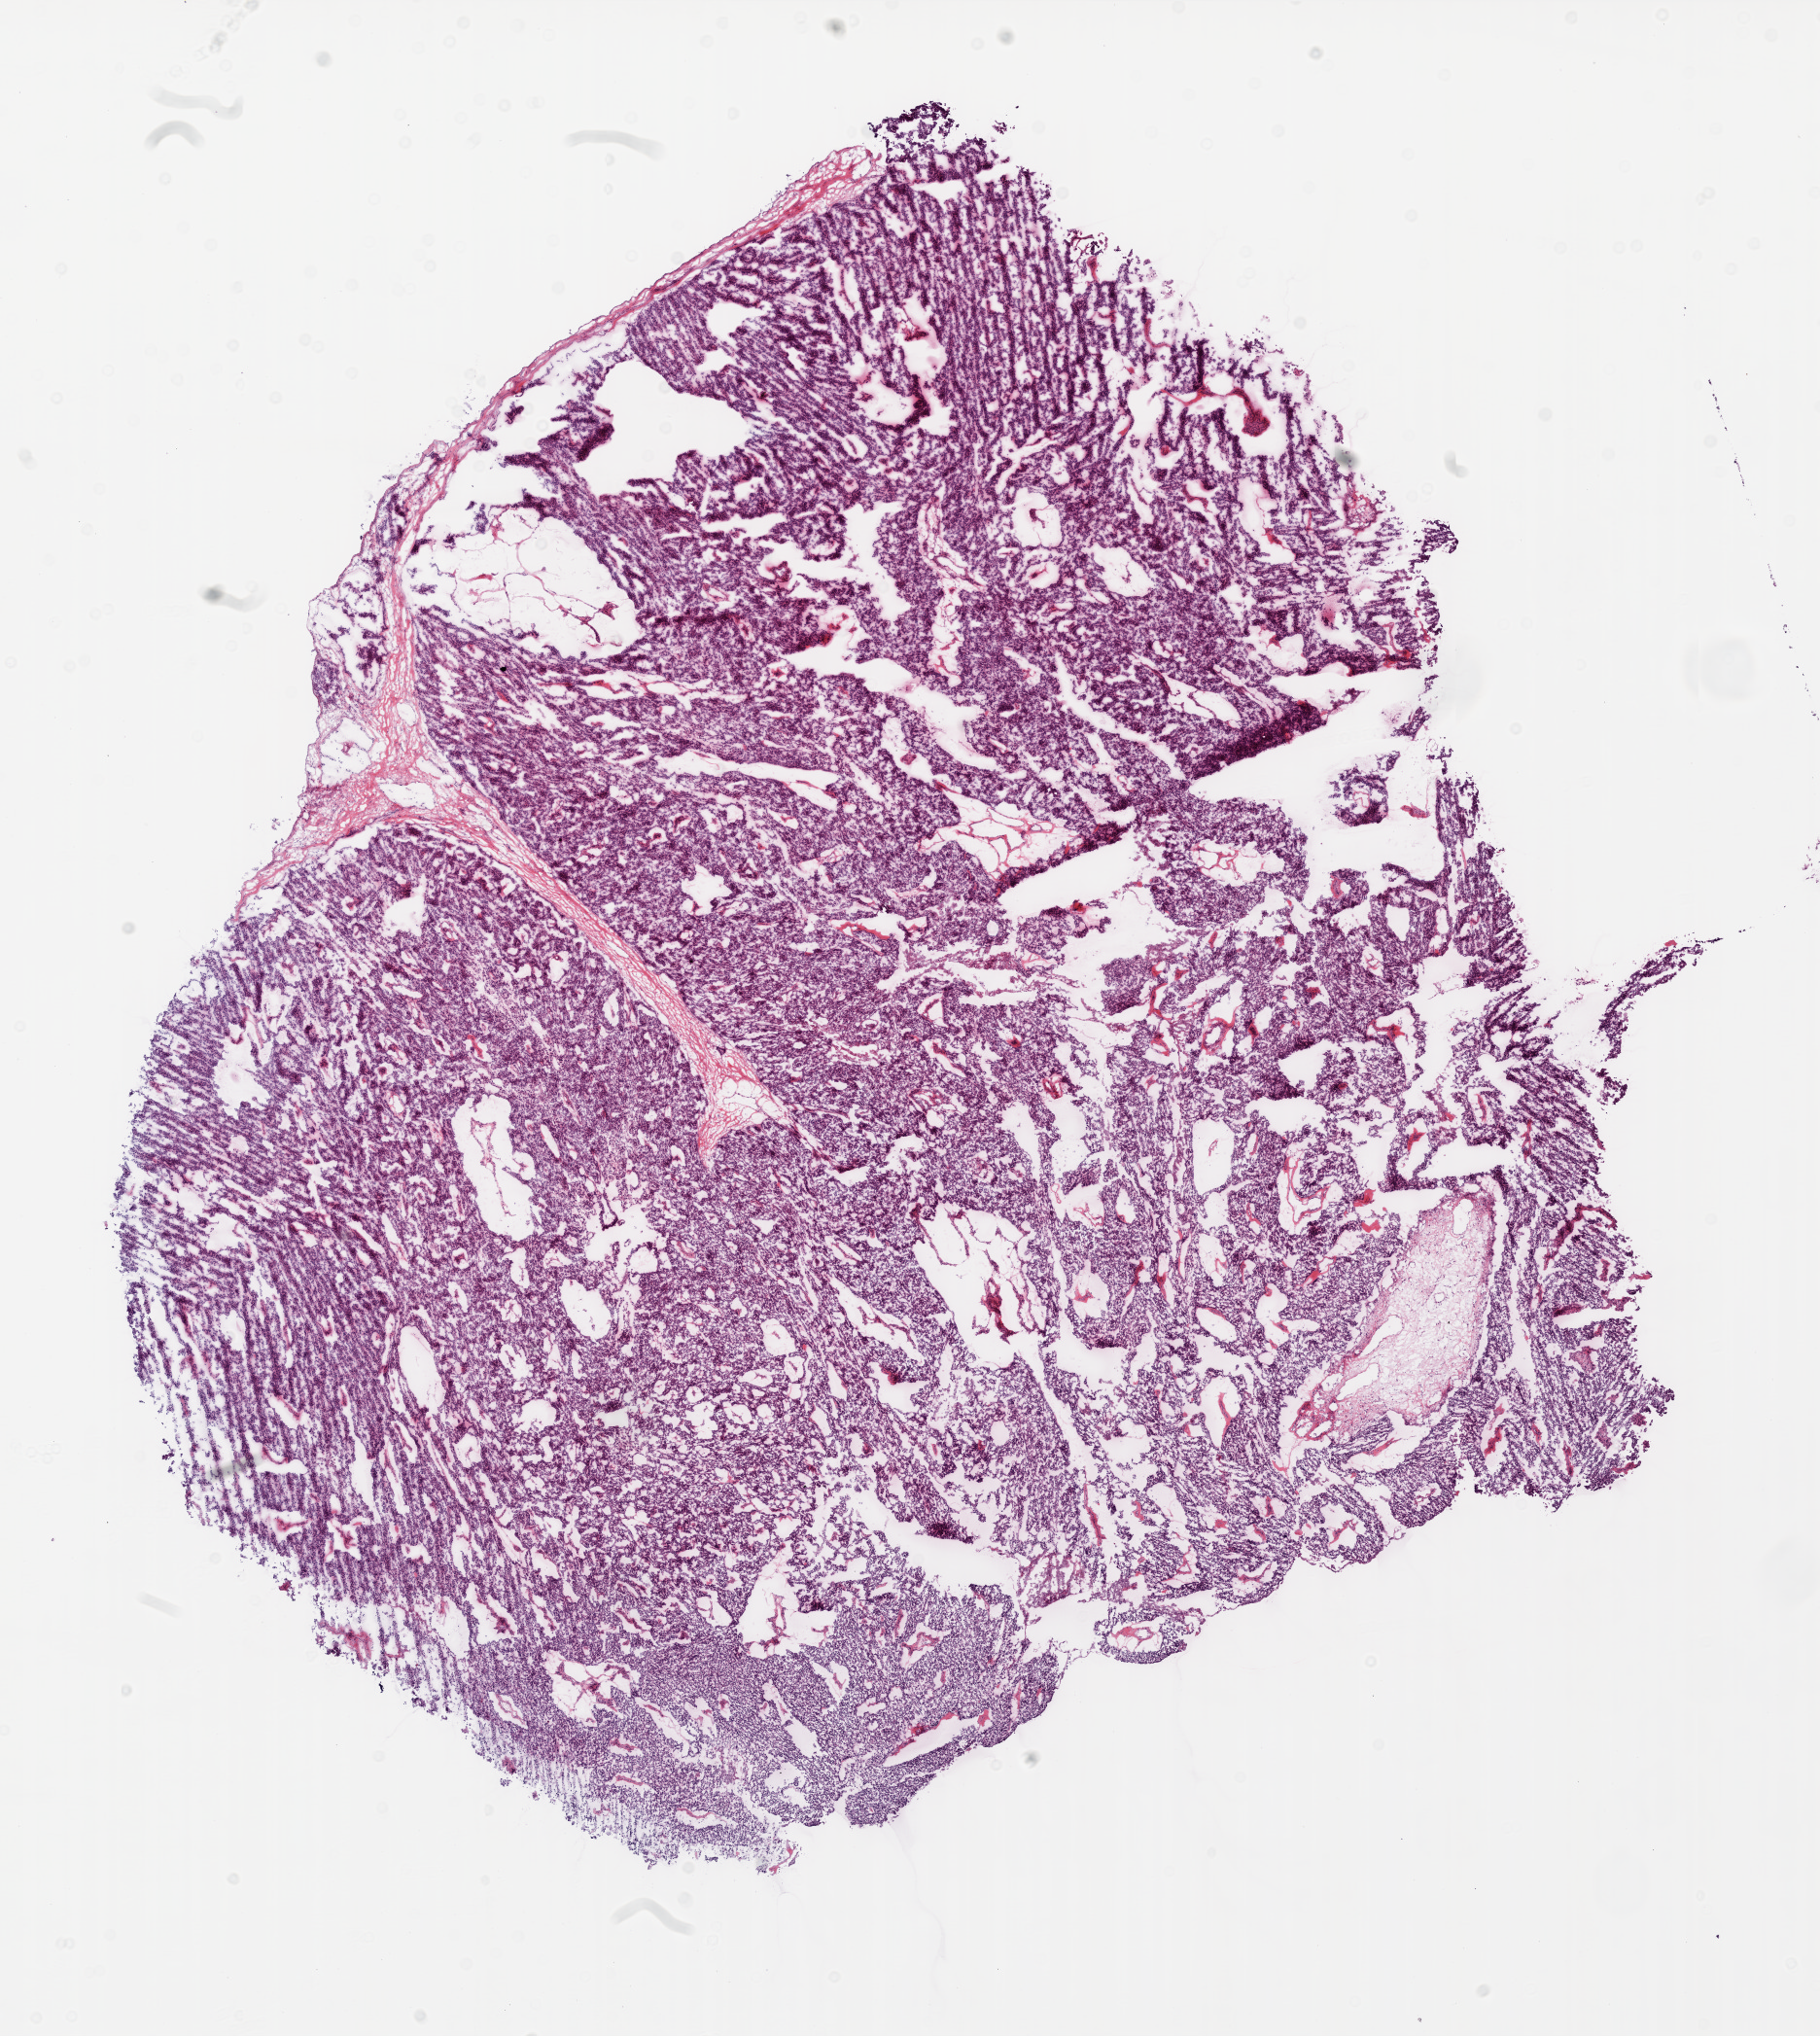
H&E-stained whole-slide image — shown as a low-resolution overview of the whole scanned area (about 15.0 x 16.8 mm, acquisition: 20x scan). Frozen section from the top of the tissue portion. Ovary, primary tumour sample. Patient: female, age at initial diagnosis 73 years.
Histologic diagnosis: Serous cystadenocarcinoma, NOS.